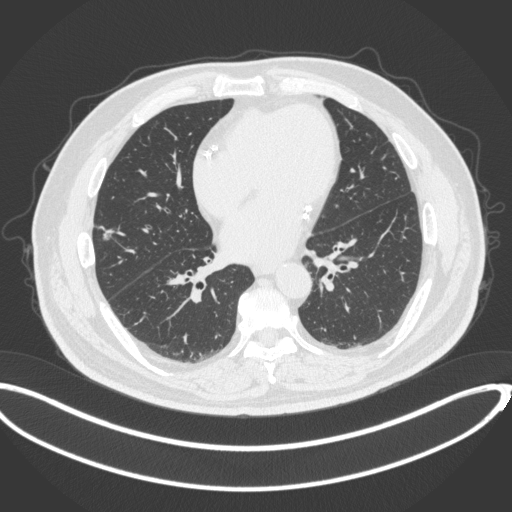
Chest CT, one axial slice. Position 139 of 342 along the scan axis. 120 kVp. Lung window (W 1500 / L -600 HU). 1 mm slice thickness. 512 × 512 image matrix, field of view 427 × 427 mm. Patient: male, 68 years. From the clinical record (not read from this slice): clinical TNM (as recorded): T1c N0 M0; histopathological grade: G2.
Outlined on this slice (bounding box drawn by a radiologist):
- lung tumour (recorded histology: adenocarcinoma): bounding box <99,225,115,241> (left, top, right, bottom; pixels)